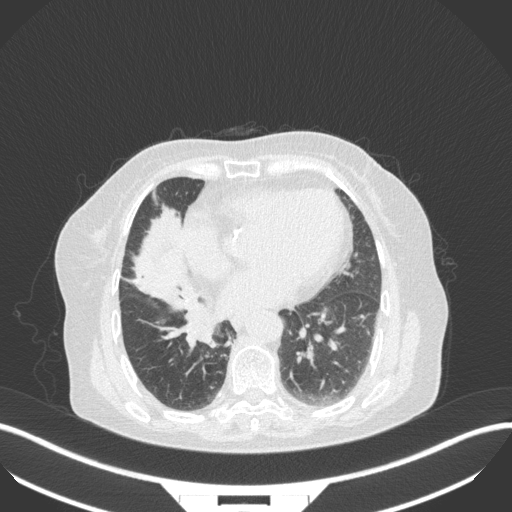
Chest CT, one axial slice; slice 121 of 329 in the series (ordered by position); 120 kVp; lung window (W 1500 / L -600 HU); 1 mm slice thickness; 512 × 512 image matrix, field of view 400 × 400 mm. Female patient, age 75 years. Case-level facts recorded for this patient, not image findings: clinical TNM (as recorded): T1b N0 M1a; histopathological grade: G1.
Structures marked on this image (rectangle marked by the reading radiologist):
- lung tumour (recorded histology: squamous cell carcinoma): box from (x=185, y=305) to (x=218, y=351) px